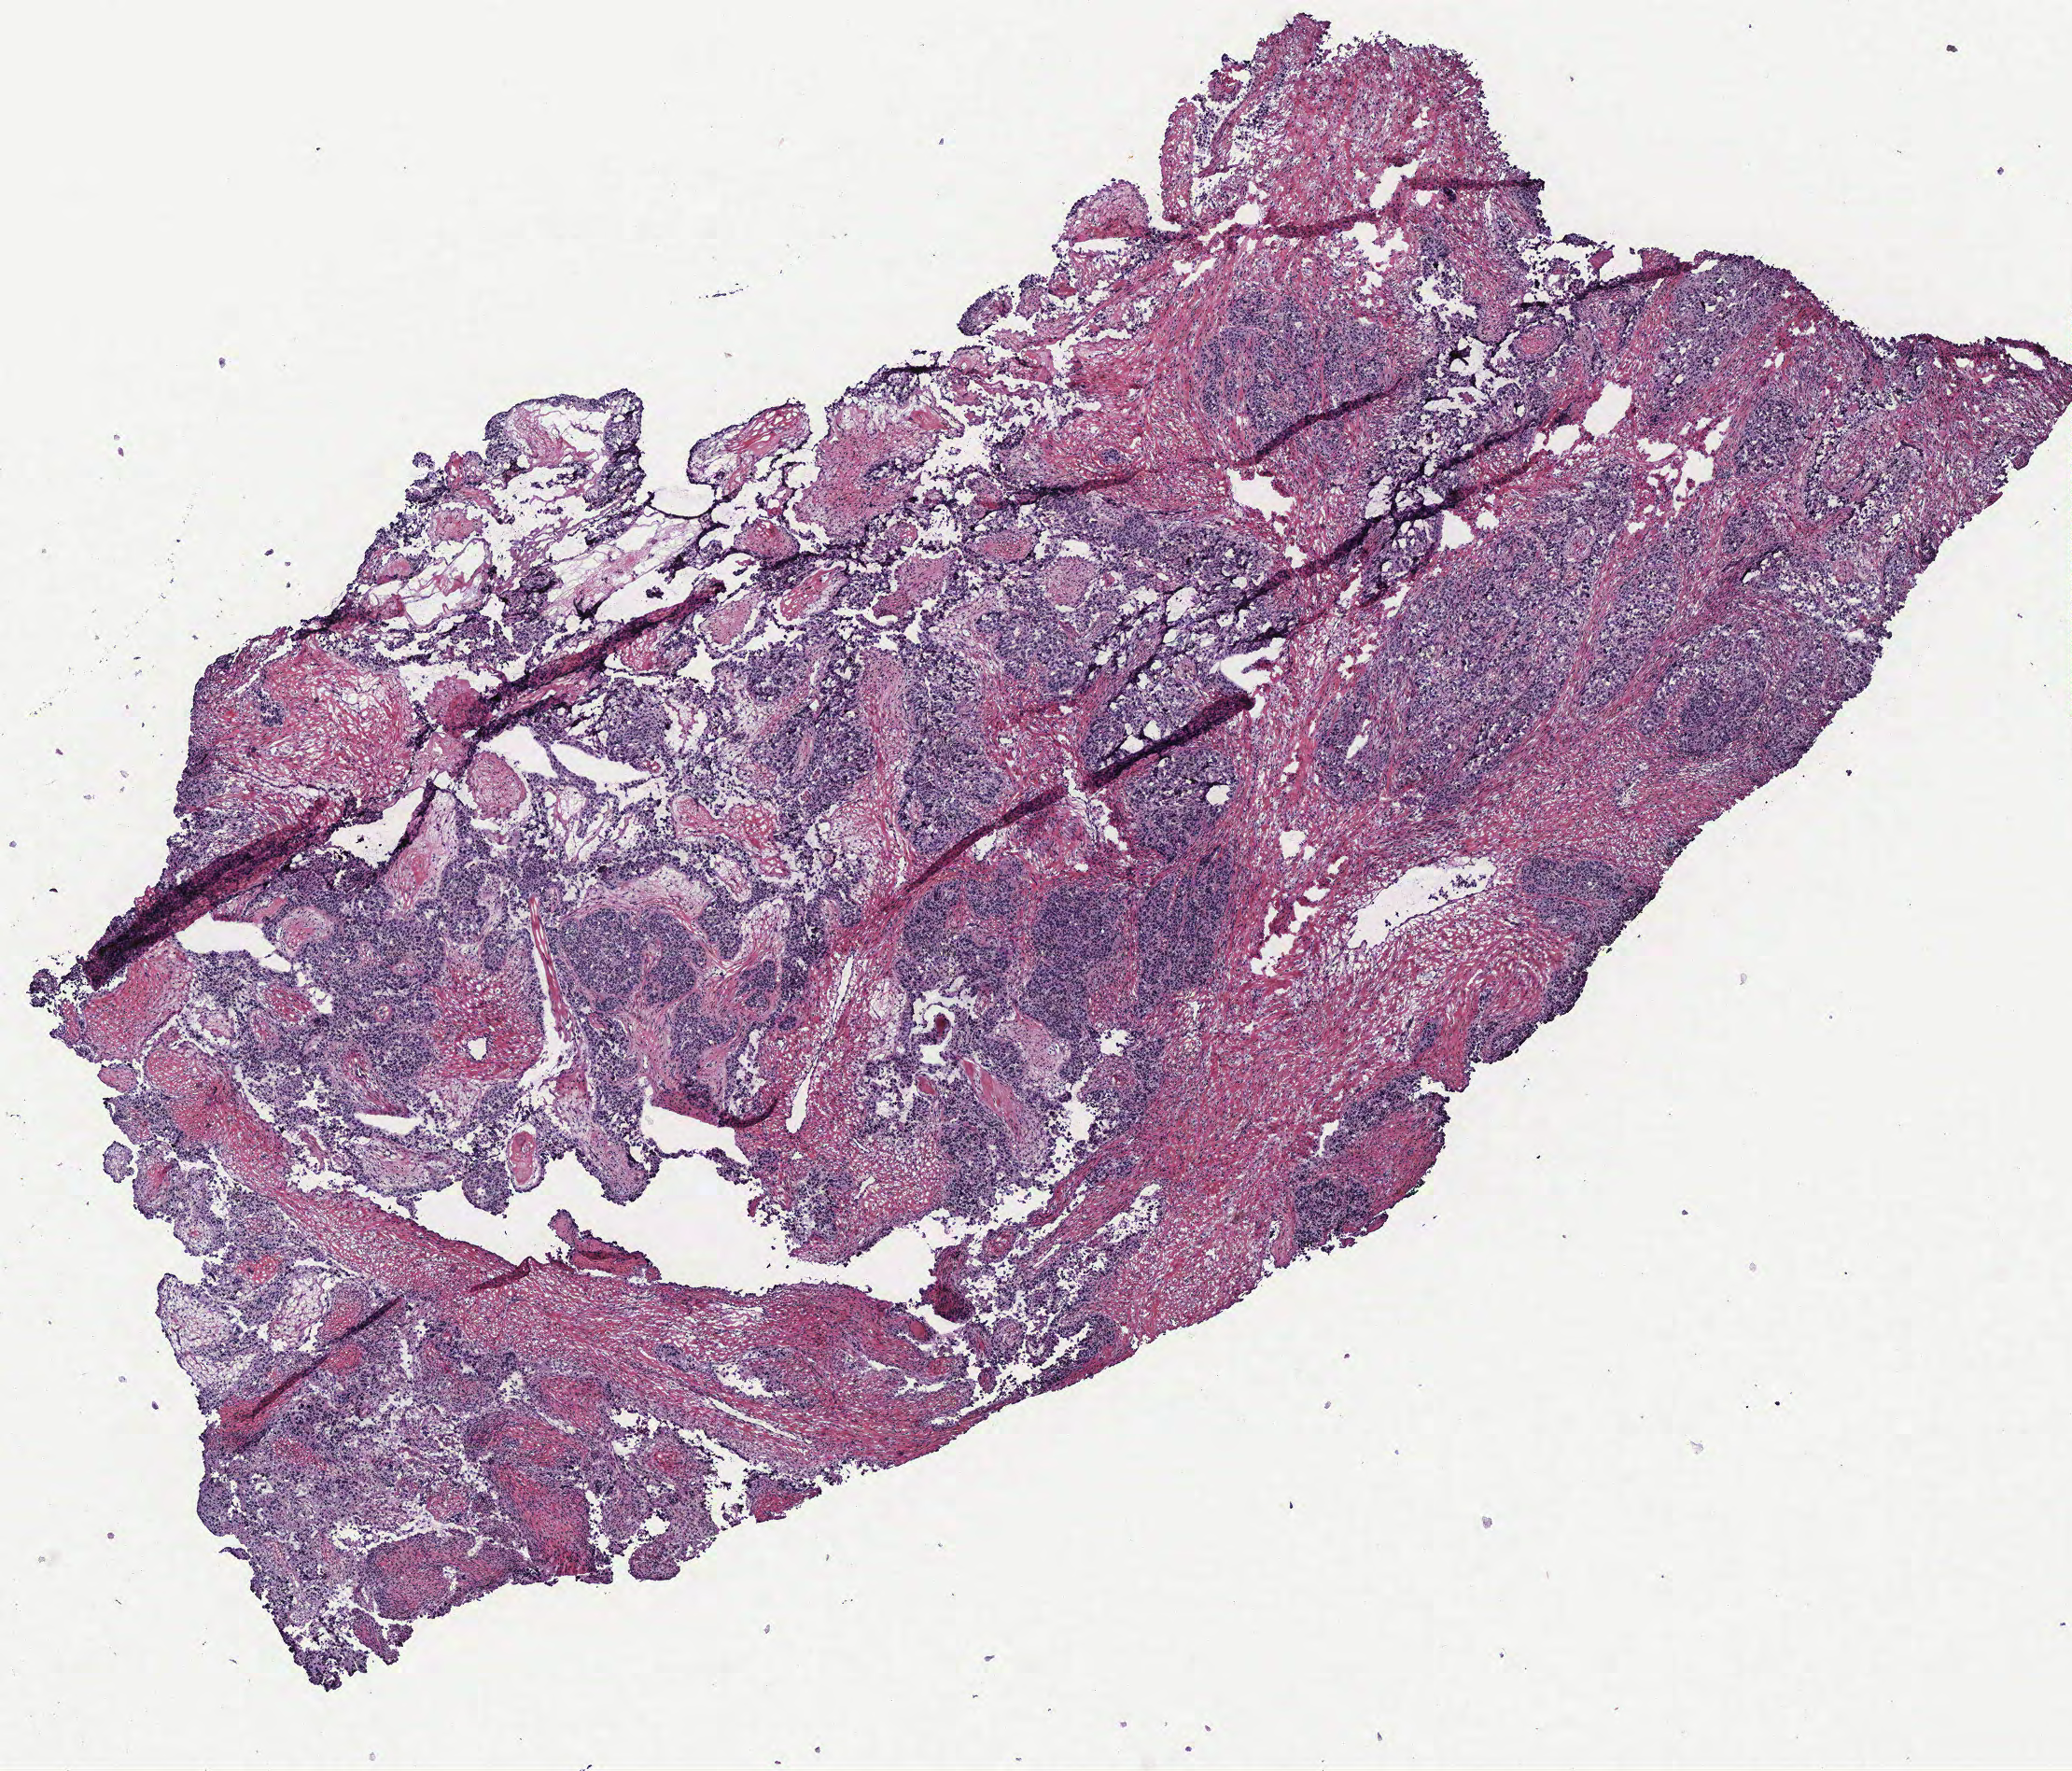
H&E whole-slide image — low-resolution overview of the scanned area, about 8.9 x 7.6 mm; ovary, tissue type not recorded.
* patient diagnosis (cohort enrolment): ovarian cancer (ovary)